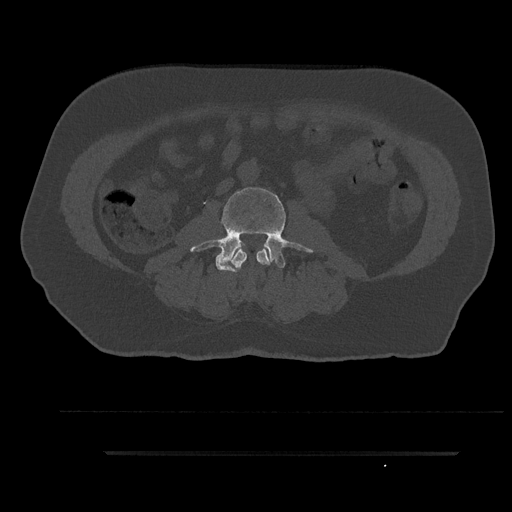
CT including the spine, one axial slice; reconstruction kernel Br40s/3; 120 kVp; bone window (W 1800 / L 400 HU); 0.5 mm slice thickness; 512 × 512 image matrix, field of view 432 × 432 mm. Male patient, age 63 years. Case-level facts recorded for this patient, not image findings: primary cancer: renal; vertebrae with lytic lesions (as recorded): T8.
Annotated regions visible in this slice (semi-automatic segmentation, software-assisted and operator-edited):
- L2 vertebra: box from (x=231, y=249) to (x=270, y=272) px
- L3 vertebra: (x=190, y=185)–(x=312, y=272)